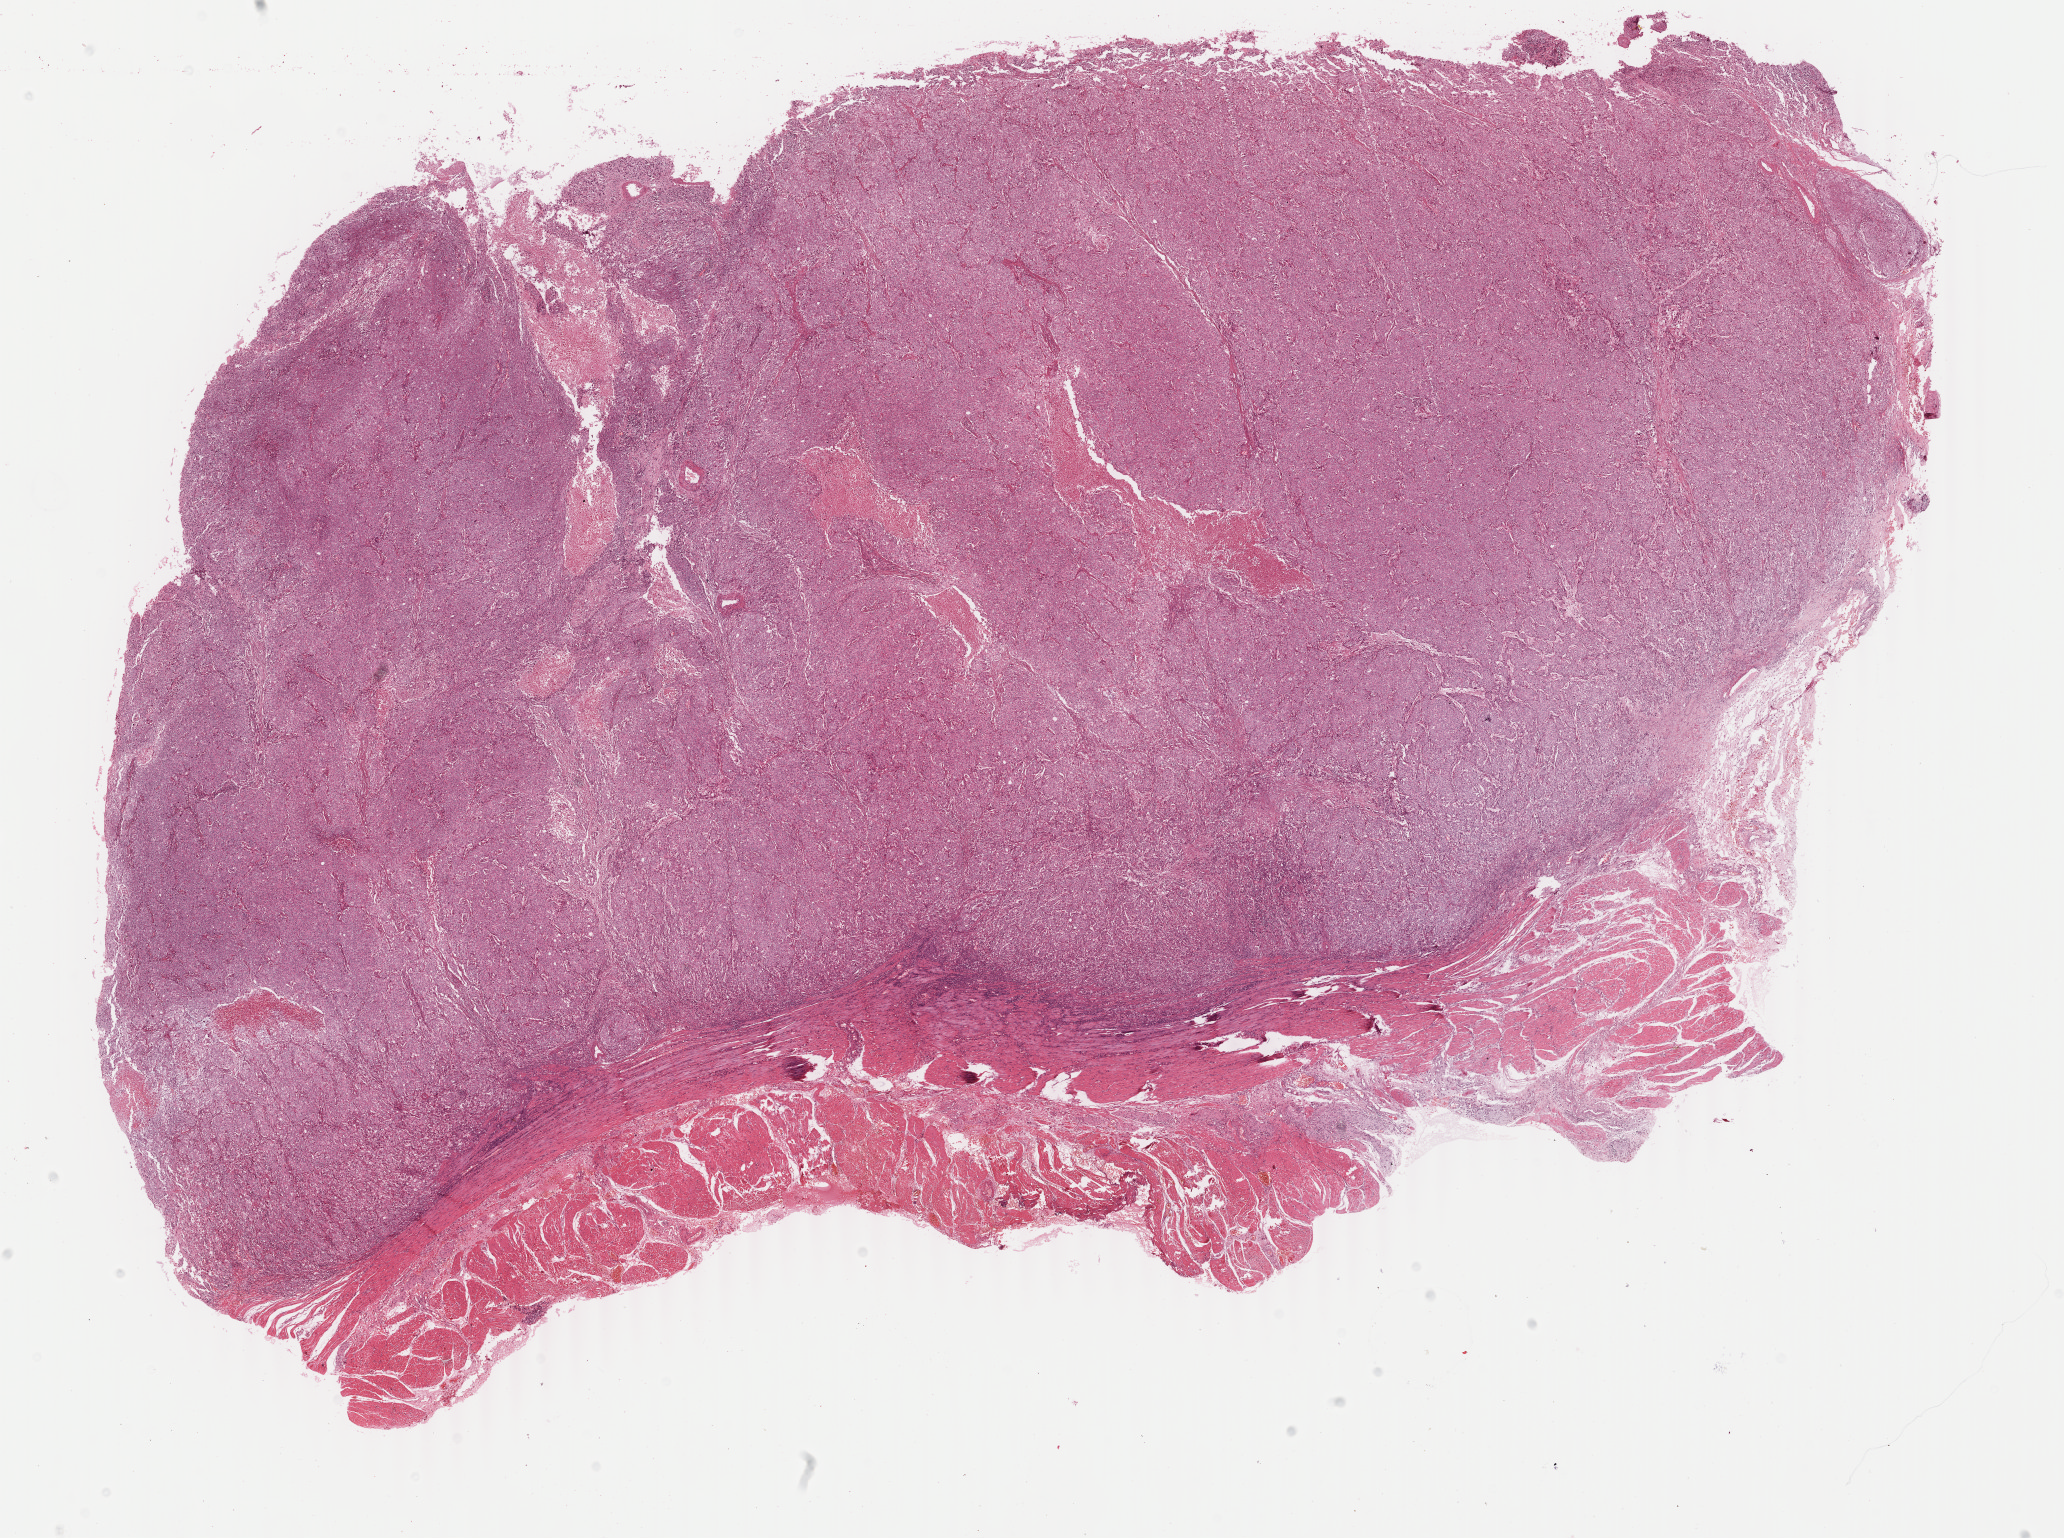
Digitized Hematoxylin and eosin (H&E) stained tissue section (whole slide) — a low-resolution overview of the entire scanned area, about 16.4 x 12.2 mm; FFPE section; sample: primary tumour, esophagus. Male patient; age at initial diagnosis 44 years. Histologic grade: G2 (moderately differentiated).
- AJCC pathologic stage: IIA
- pathologic diagnosis: Squamous cell carcinoma, NOS